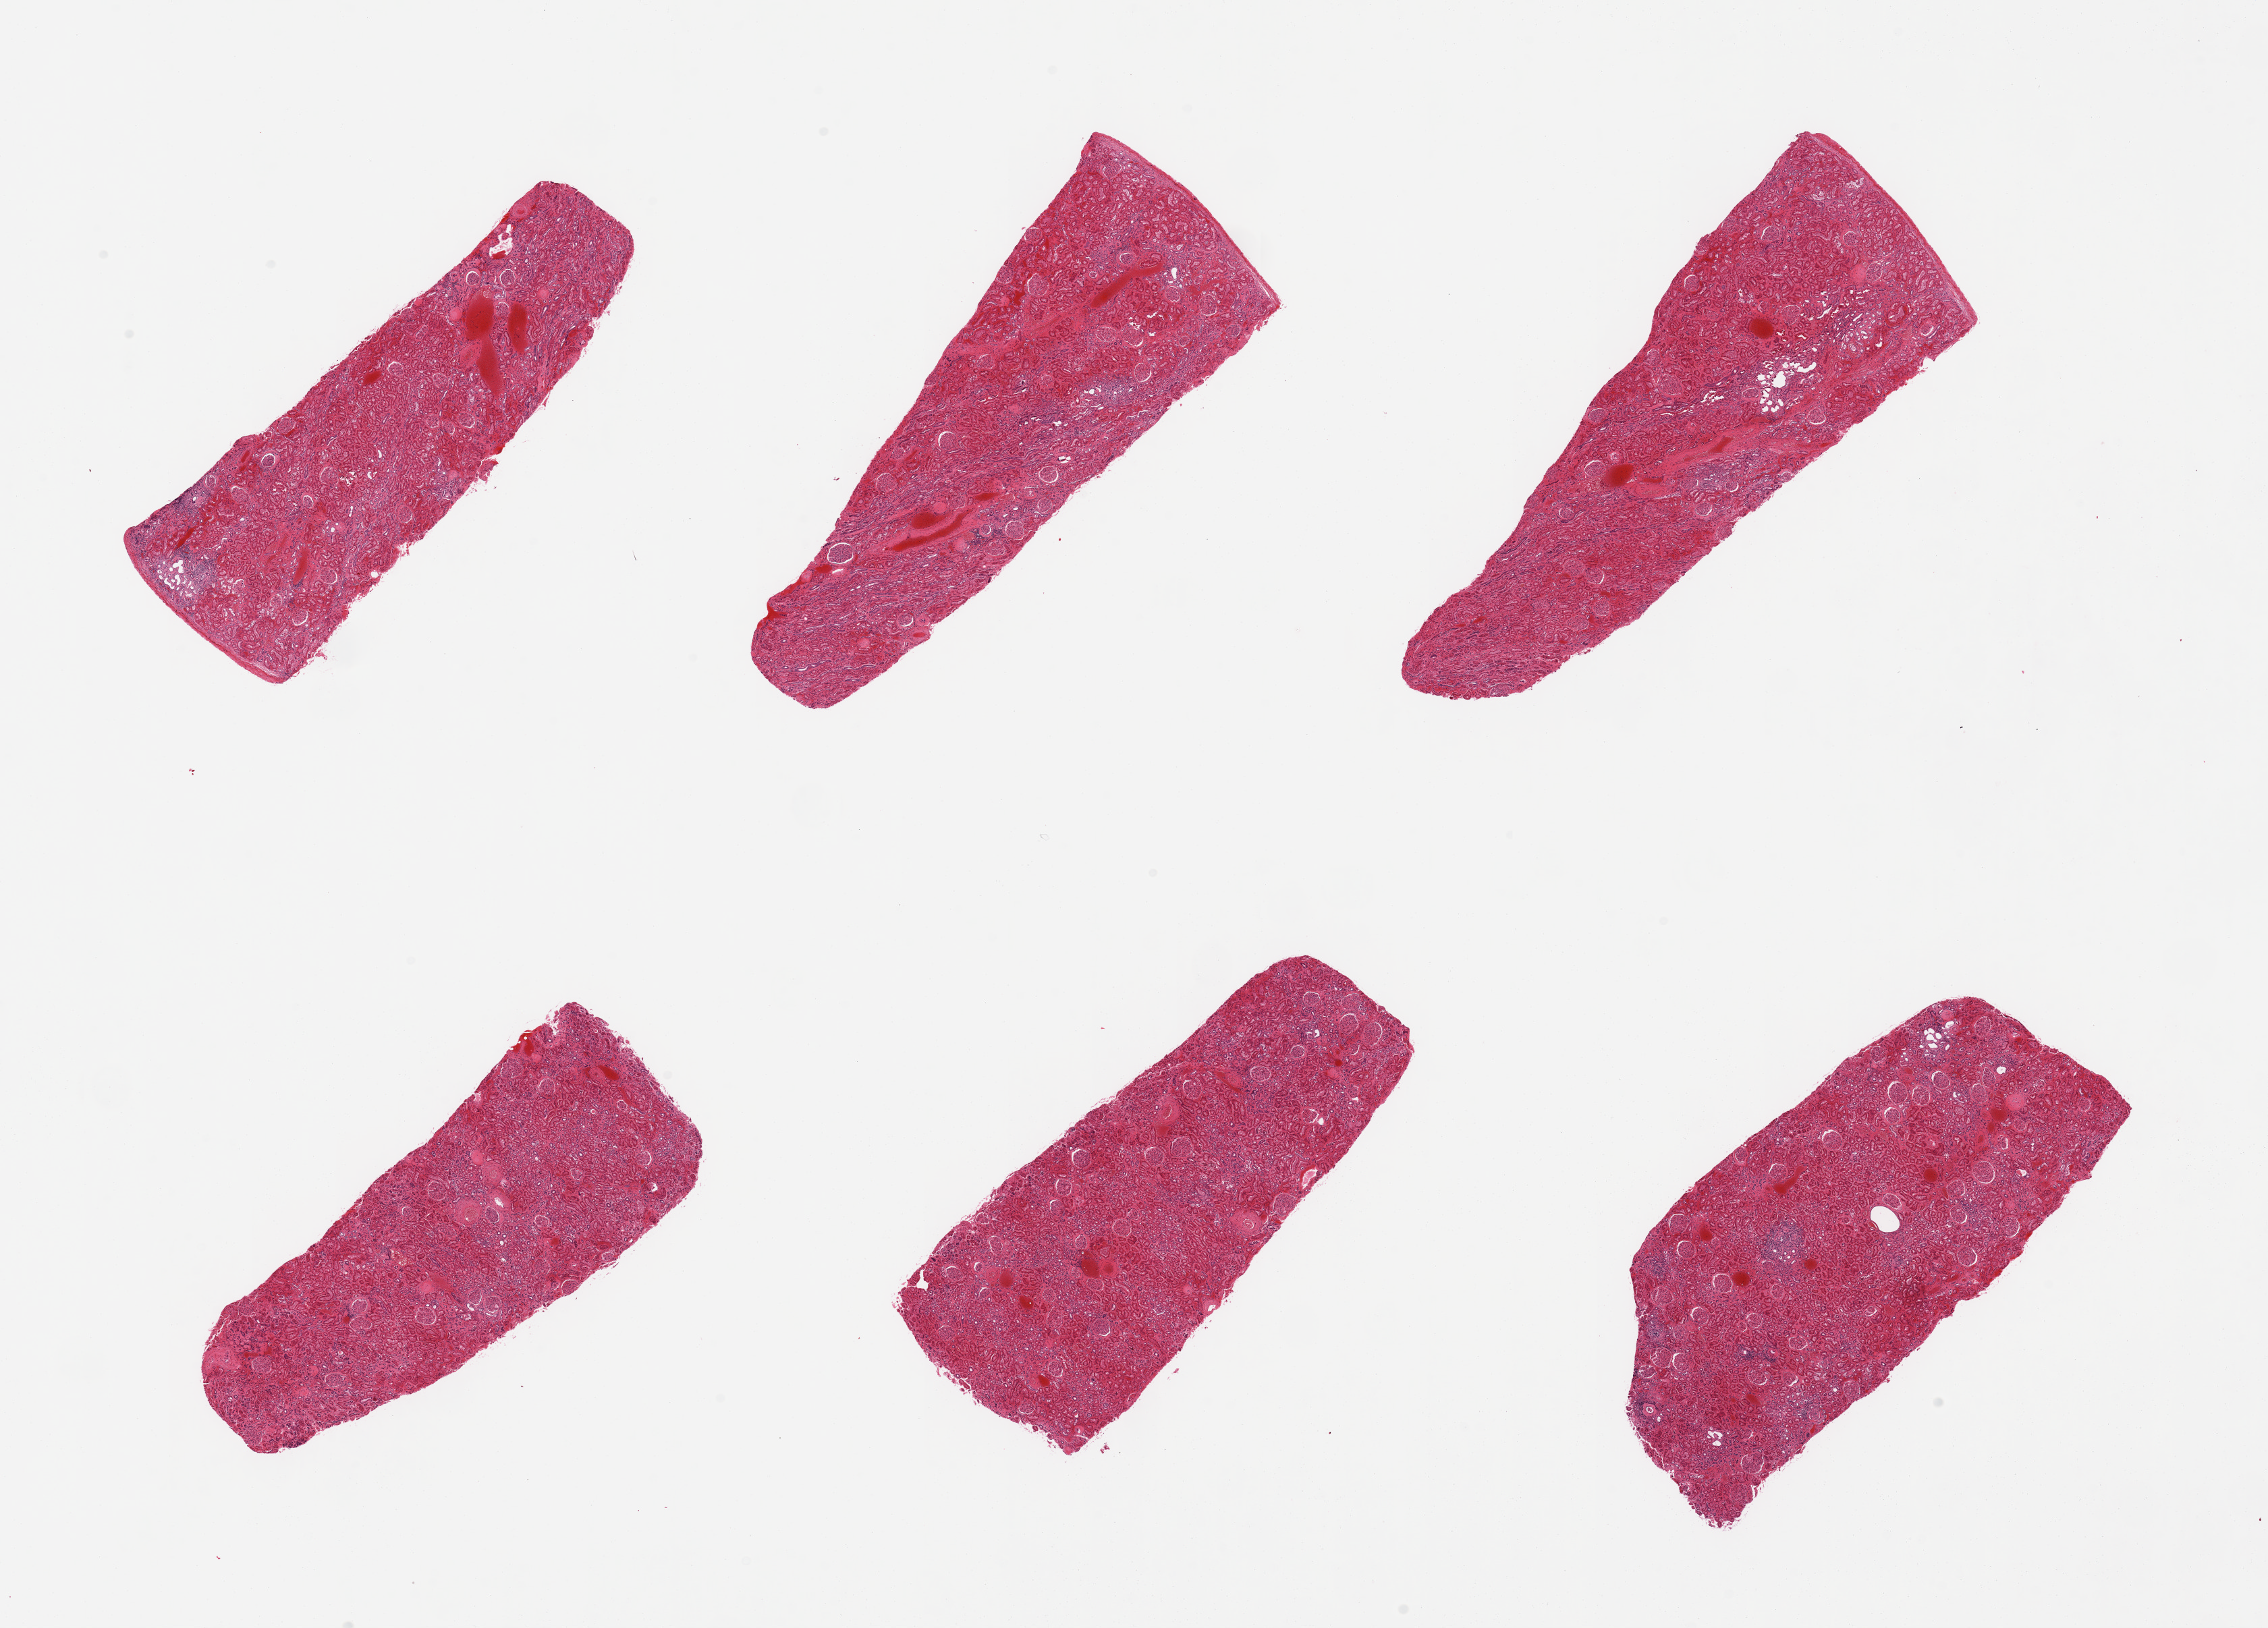
Whole-slide image, hematoxylin and eosin (H&E) stain, shown as a low-resolution overview of the whole scanned area (about 26.6 x 19.1 mm, acquisition: 20x scan); PAXgene-fixed paraffin-embedded (PFPE) section; target tissue: renal cortex; tissue donor sample.
Reviewer comment on this tissue sample: 6 pieces, glomeruli present, moderately congested.